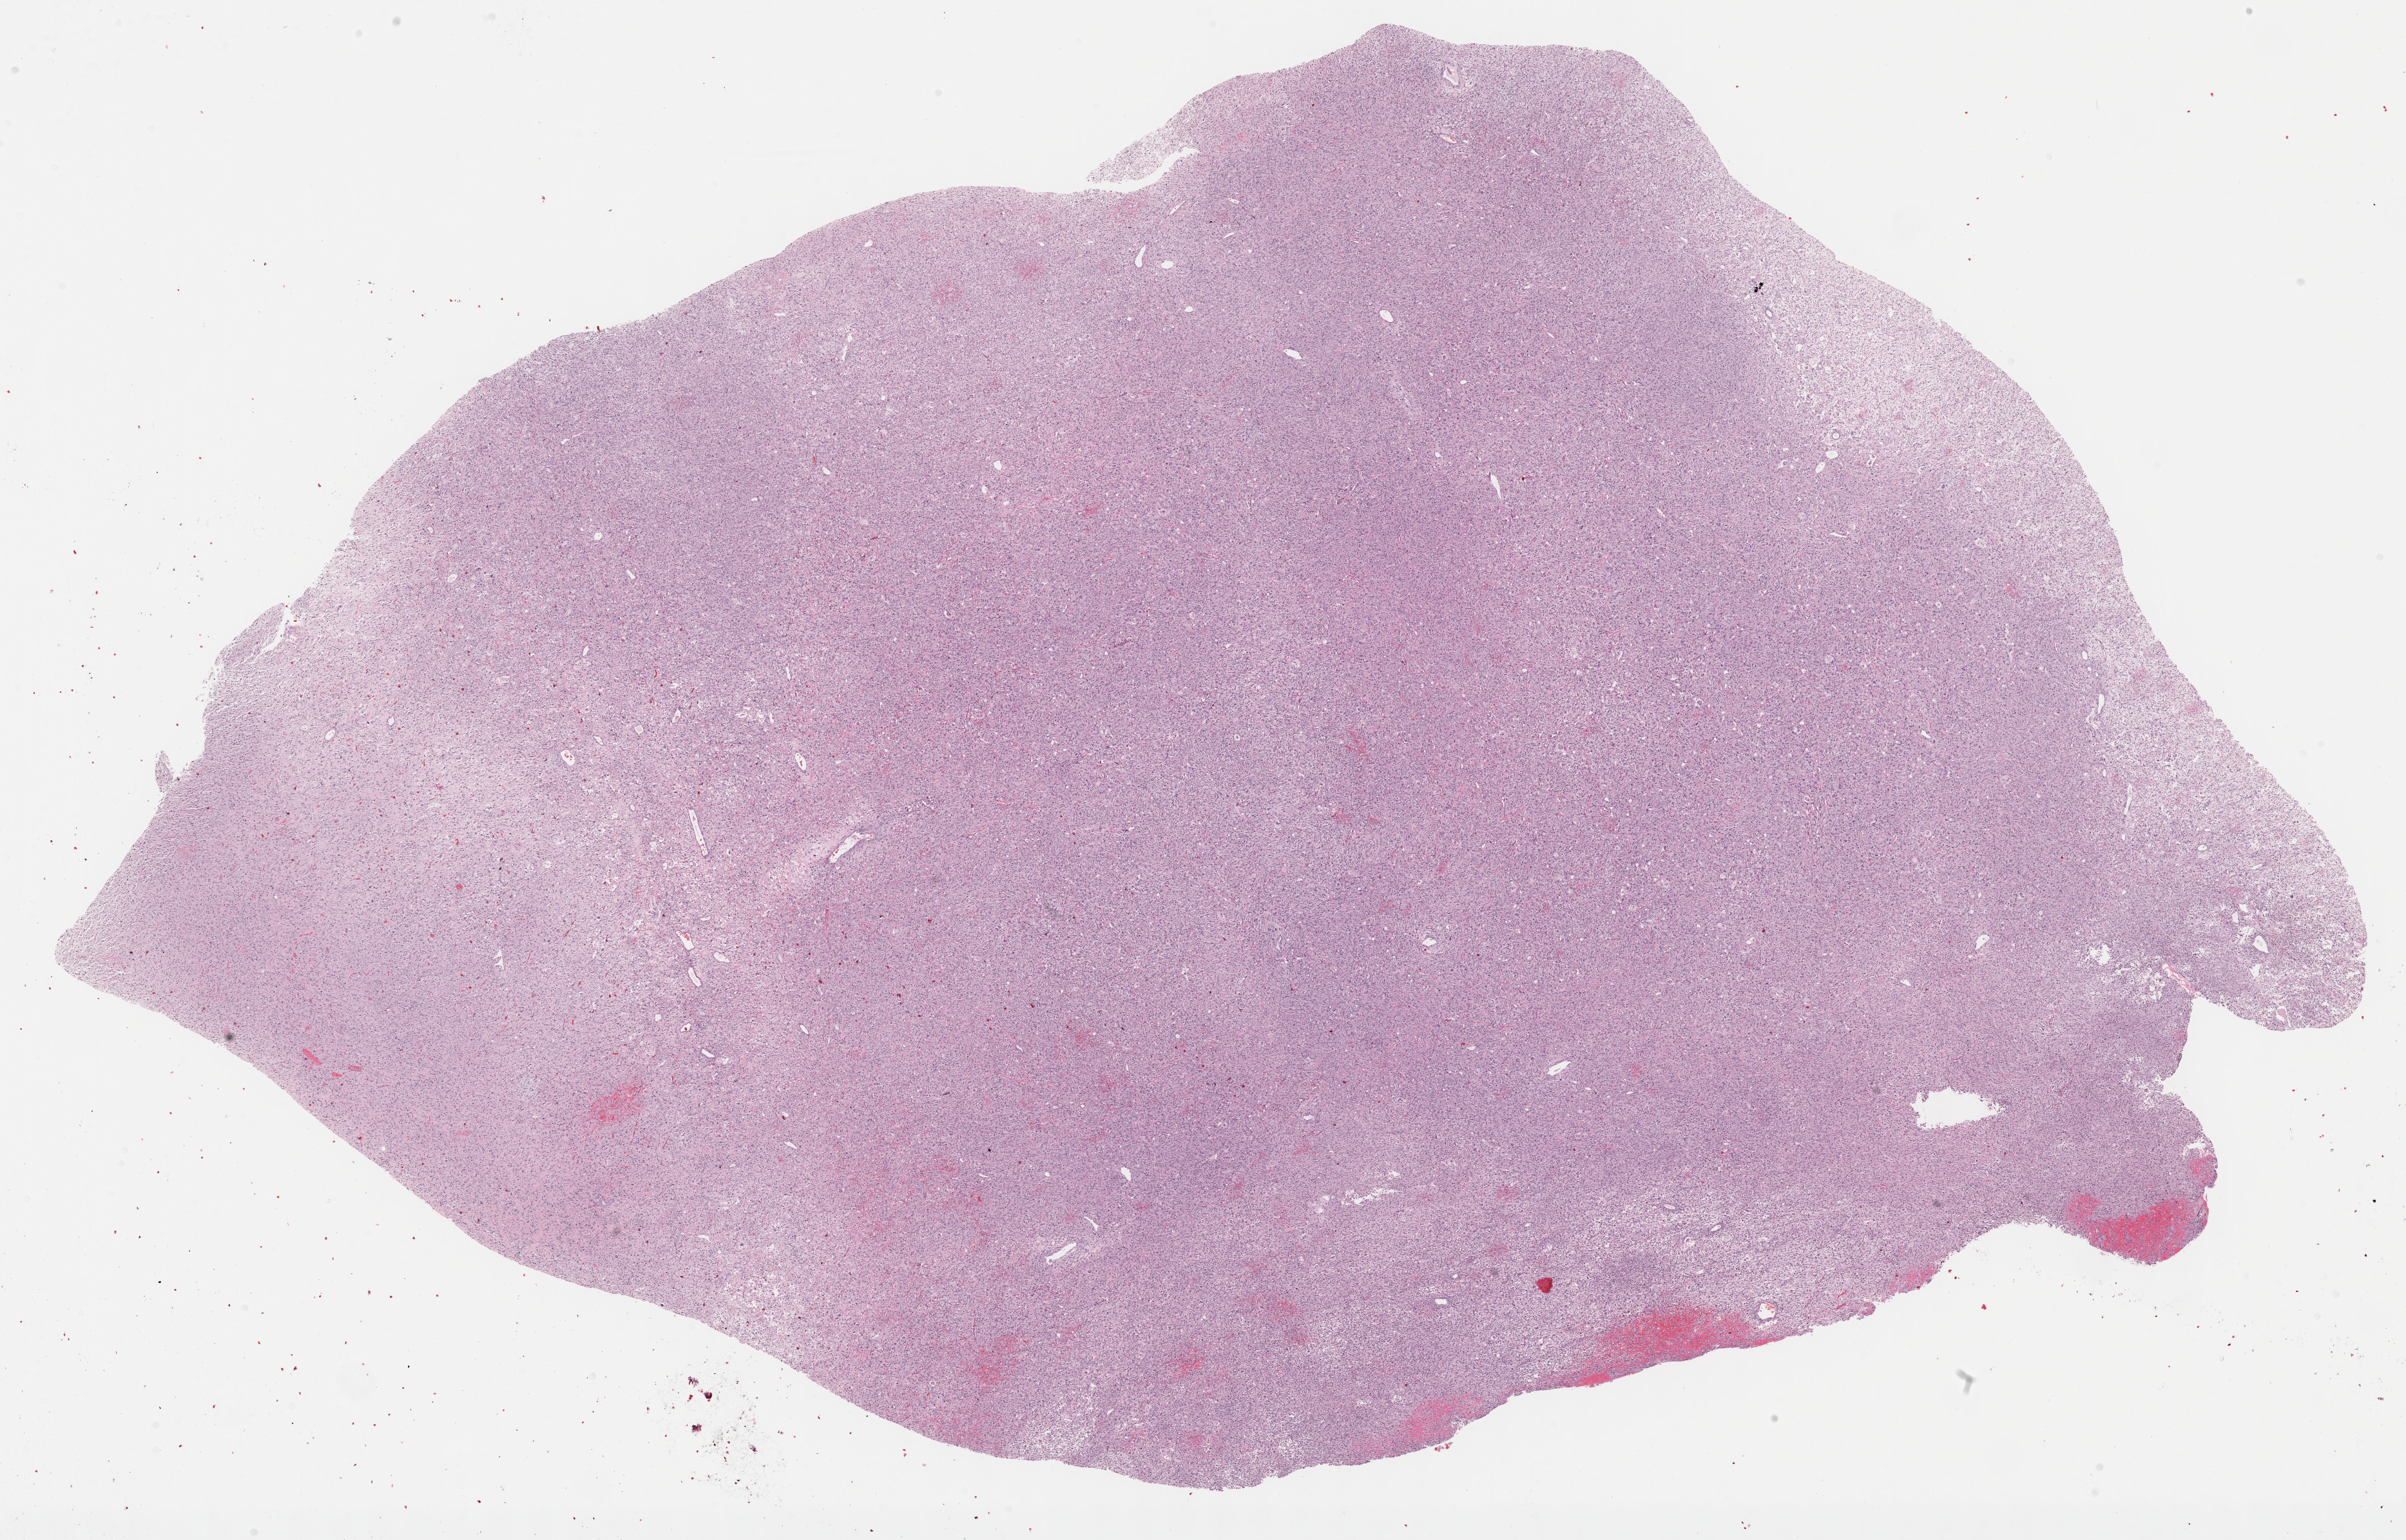
Digitized Hematoxylin and eosin (H&E) stained tissue section (whole slide), whole scanned area (about 30.2 x 19.3 mm, slide scanned at 40x) shown as a low-resolution overview, formalin-fixed paraffin-embedded (FFPE) diagnostic section, retroperitoneum and peritoneum, primary tumour sample. Male patient; age at initial diagnosis 66 years.
• pathologic diagnosis: Dedifferentiated liposarcoma (retroperitoneum)